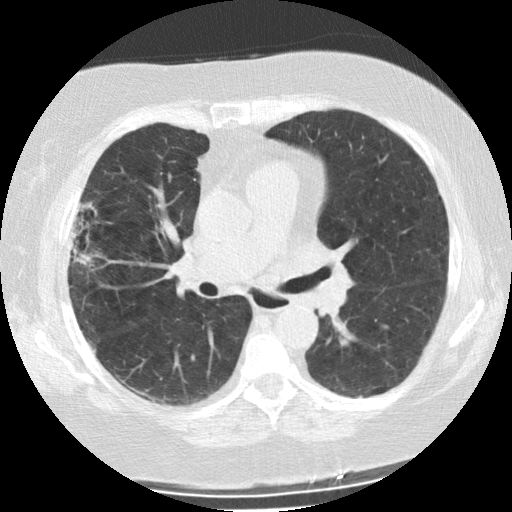
Chest CT (low-dose screening protocol), one axial image. Second annual screen. Lung window (W 1500 / L -600 HU). 2.5 mm slice thickness. Standard (soft-tissue) reconstruction kernel (STANDARD). Slice 94 of 225 in the series. 512 × 512 image matrix, field of view 320 × 320 mm. Female, age 73 years at enrolment.
Expert-annotated lung lesion, bounding box <57,200,105,276> (left, top, right, bottom; pixels). The screening reader recorded 2 non-calcified nodules or masses ≥4 mm on this exam (right upper lobe, left upper lobe); which of them this box marks is not recorded. Later outcome: lung cancer diagnosed 47 days after this screen — bronchiolo-alveolar adenocarcinoma, NOS, right upper lobe, moderately differentiated (G2), stage IIIB (AJCC 6th edition), 21 mm at pathology.